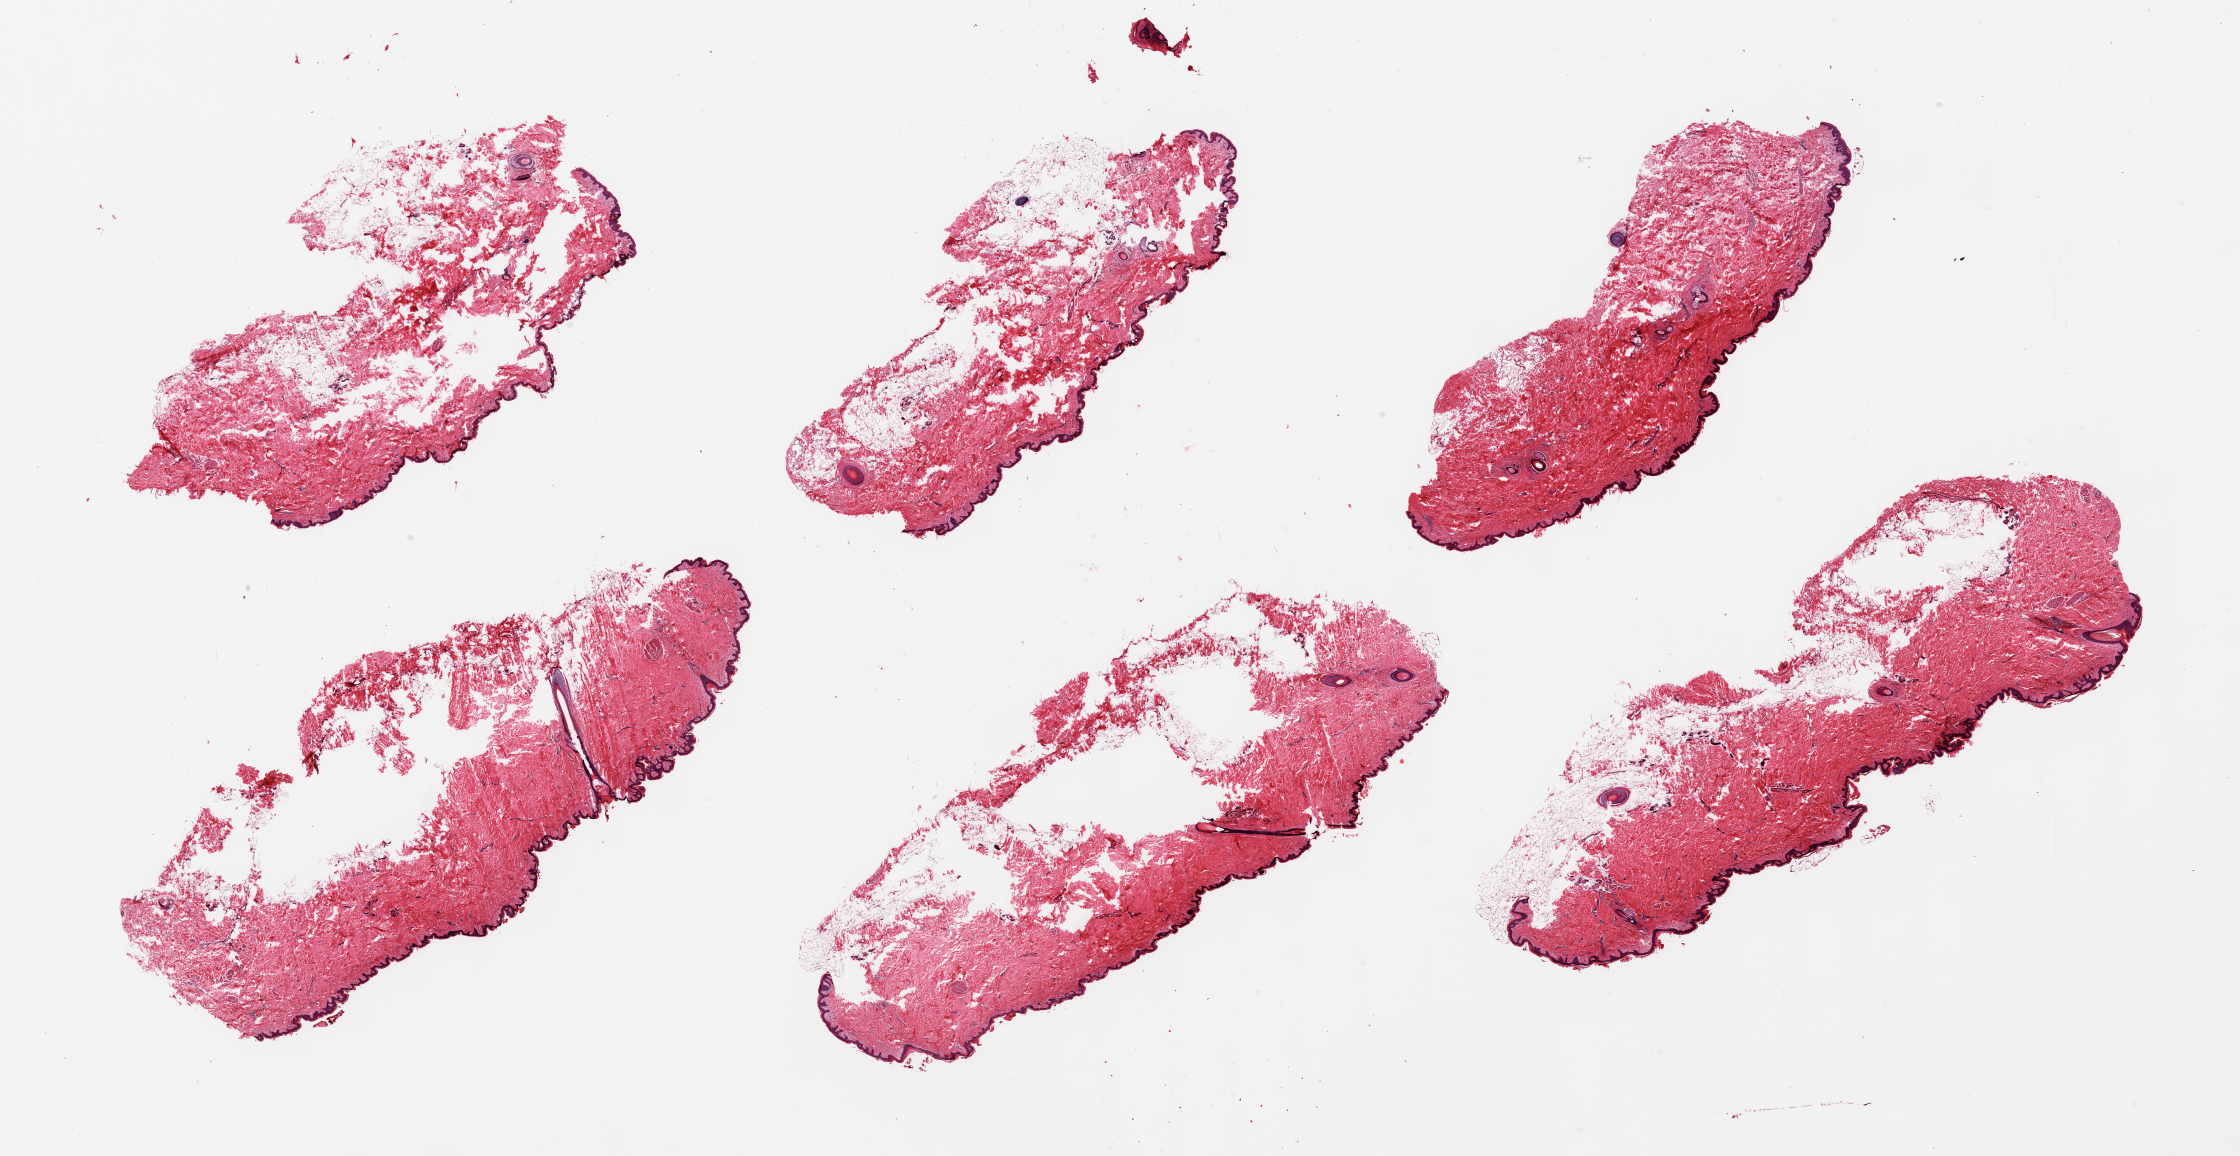
Haematoxylin and eosin whole-slide image, shown as a low-resolution overview of the whole scanned area (about 35.4 x 18.3 mm, acquisition: 20x scan), PAXgene-fixed paraffin-embedded (PFPE) section, sampled site (target tissue): skin of suprapubic region, tissue donor sample. Donor sex: female.
Review note (as recorded): 6 pieces; up to 30% dermal fat, heavily fragmented.